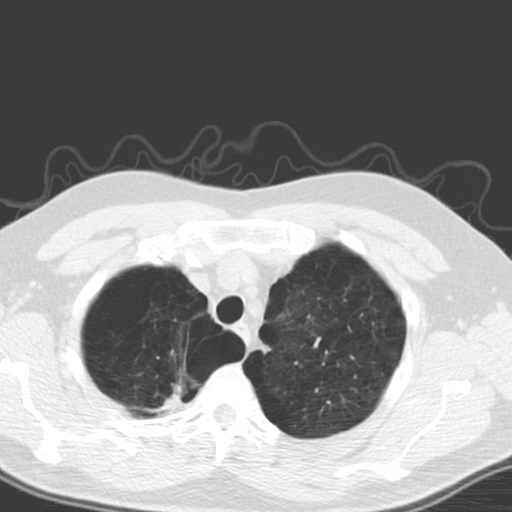
Low-dose screening chest CT, axial slice. First (baseline) screen. Lung window (W 1500 / L -600 HU). Slice 29 of 173 in the series. 512 × 512 image matrix. Male, age 56 years at enrolment.
Lesion marked by an expert reader, box from (x=137, y=354) to (x=208, y=424) px. Reader record for this screening exam (exam-level; its link to the box is not recorded): non-calcified nodule or mass ≥4 mm, right upper lobe, 20 × 12 mm, spiculated (stellate) margins, soft tissue attenuation. Official screen result: positive, change unspecified: nodule(s) >= 4 mm or enlarging nodule(s), mass(es), or other non-specific abnormalities suspicious for lung cancer. Participant outcome: lung cancer diagnosed 205 days after this screen — large cell carcinoma, NOS, right upper lobe, poorly differentiated (G3), stage IA (AJCC 6th edition), 18 mm at pathology.